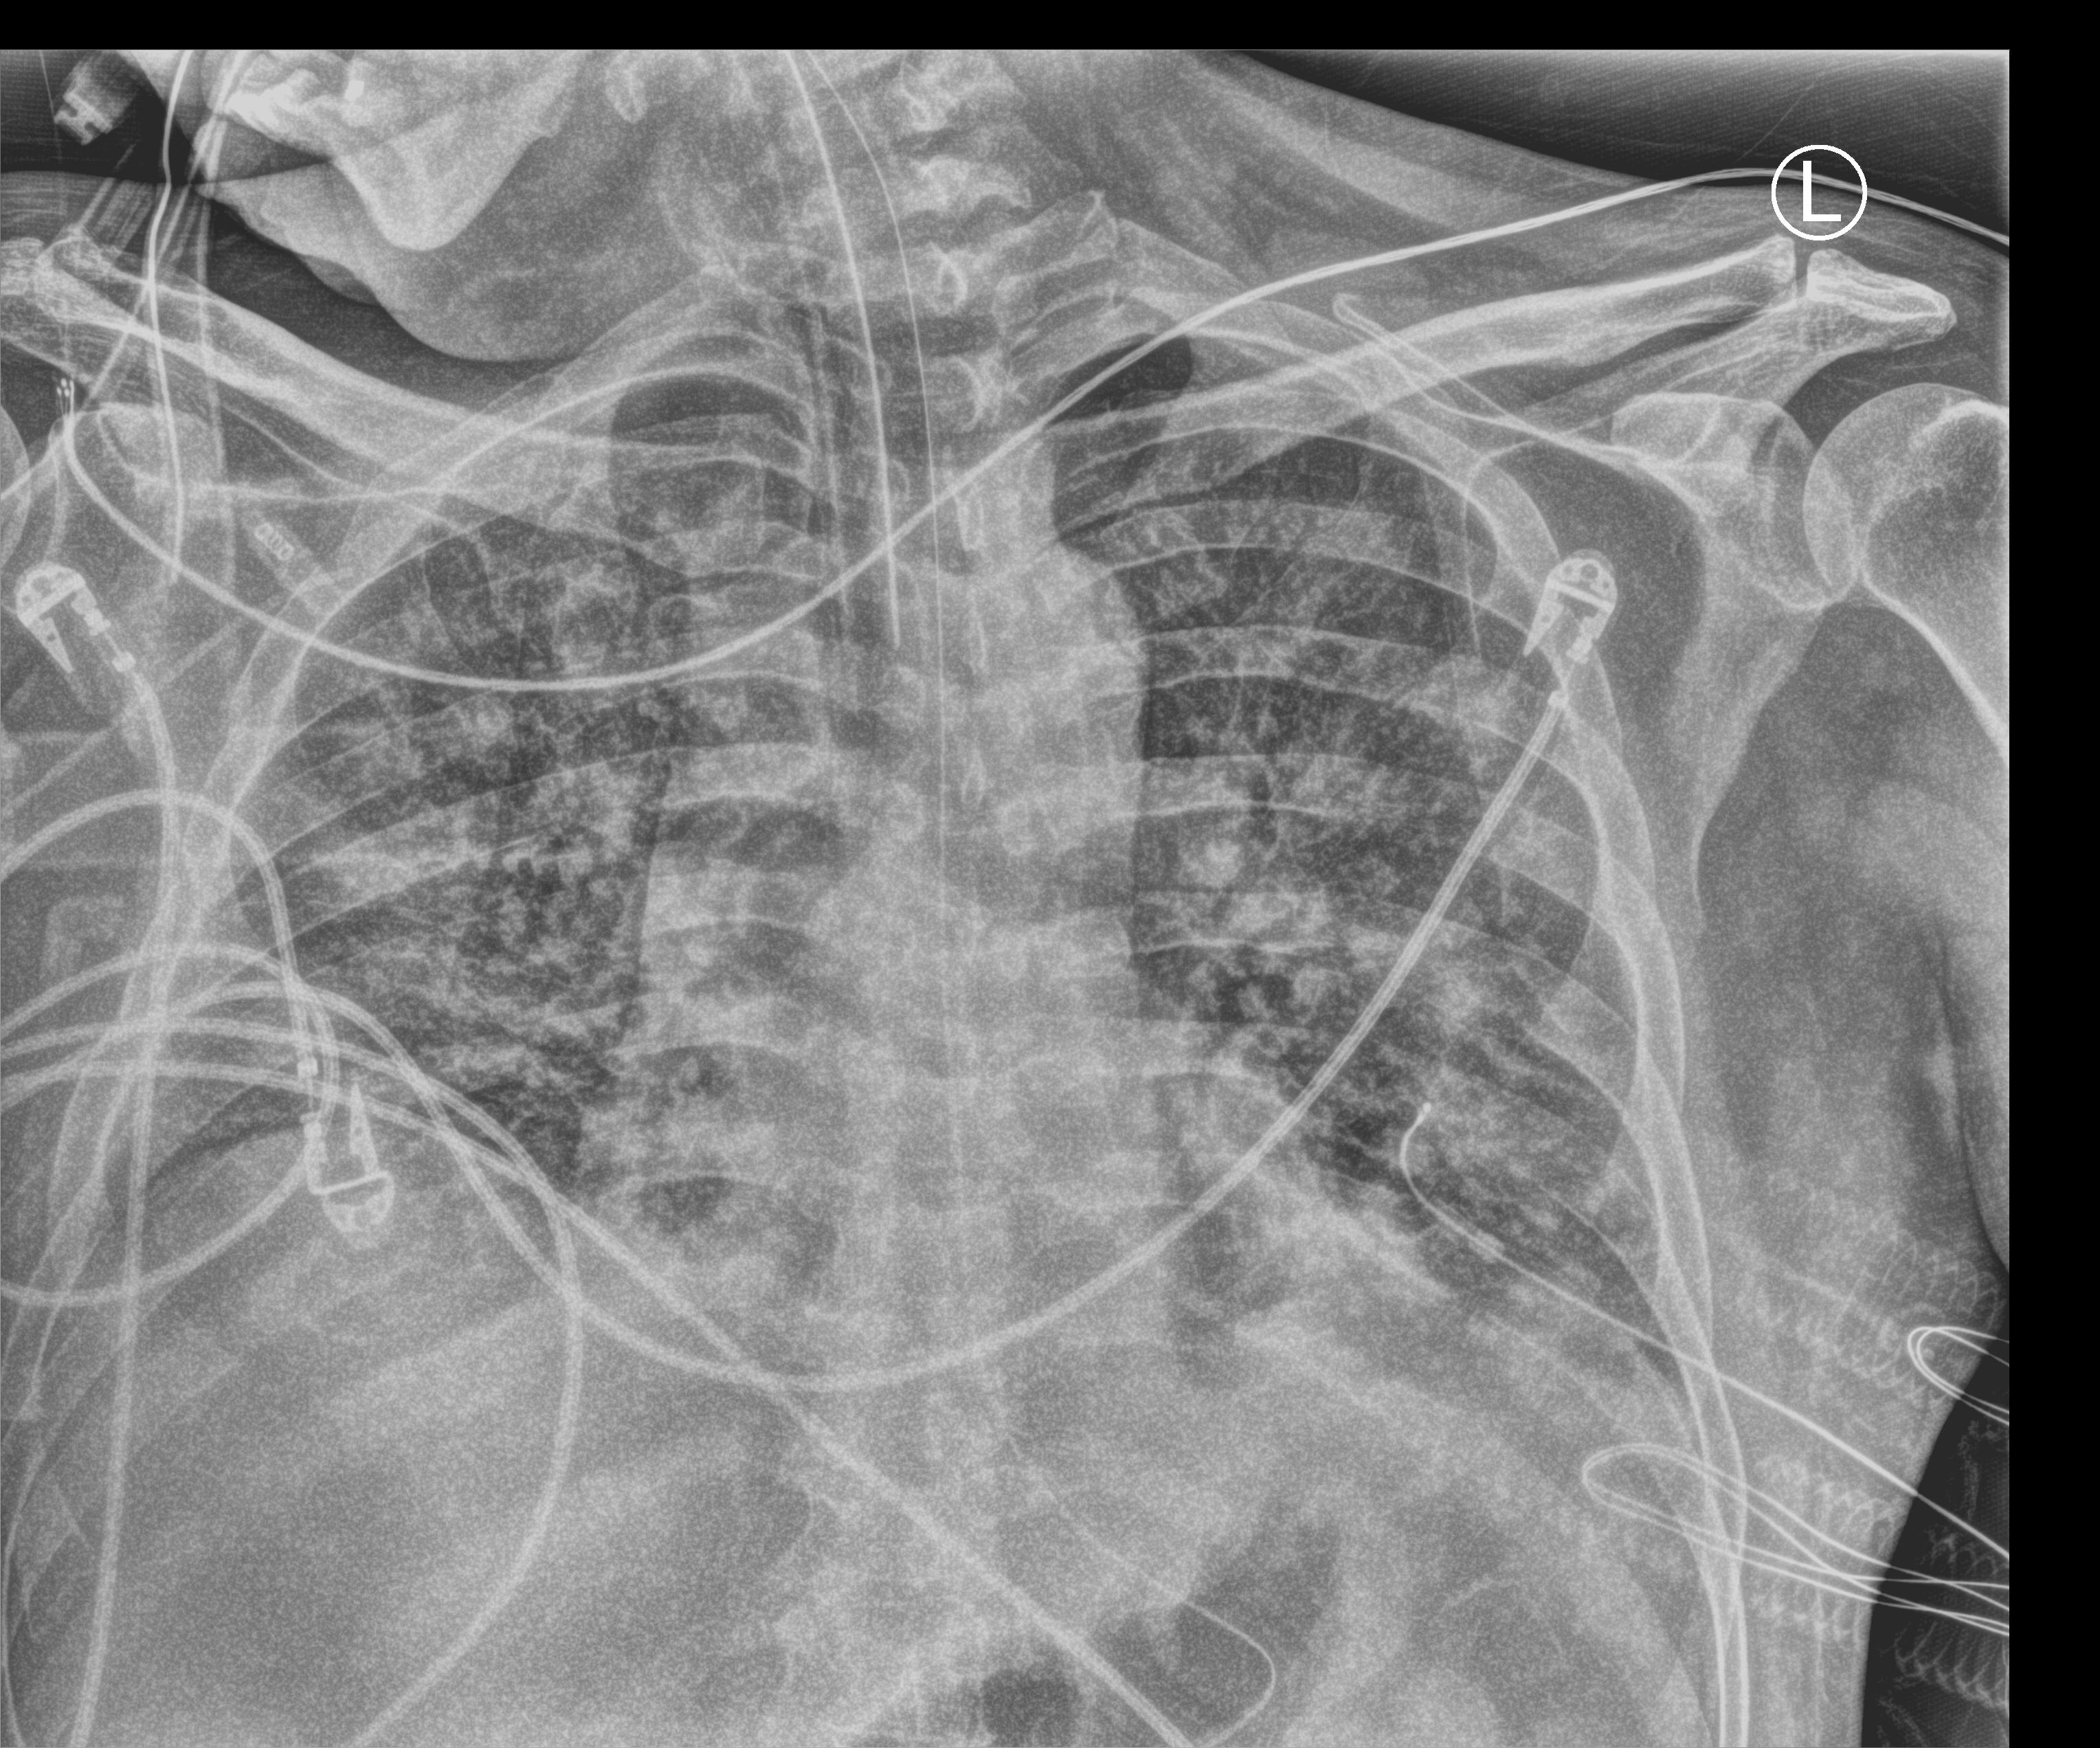
Bedside chest radiograph (computed radiography); anteroposterior (AP) projection. Male patient hospitalised with COVID-19, age 18–59 years.
From the hospital-stay record, not from the radiograph (when in the stay this image was taken is not recorded): mechanically ventilated during this hospital stay: yes.